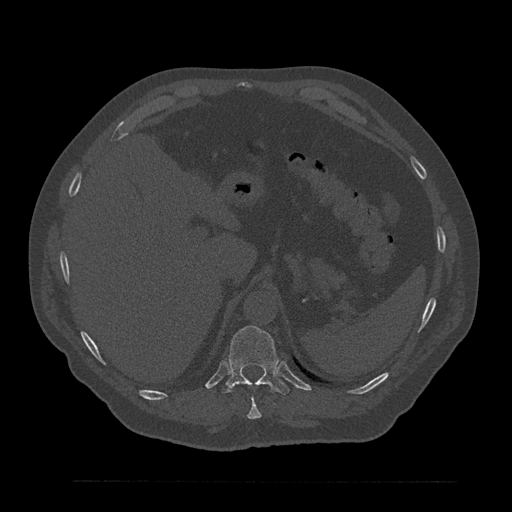
CT including the spine, one axial slice. Reconstruction kernel Br40s/3. Bone window (W 1800 / L 400 HU). 0.5 mm slice thickness. 512 × 512 image matrix, field of view 430 × 430 mm. Male patient, age 61 years. From the clinical record (not read from this slice): primary cancer: prostate.
Annotated regions visible in this slice (semi-automatically segmented with operator editing):
- T10 vertebra: bounding box (x1, y1, x2, y2) in pixels: (247, 397, 262, 419)
- T11 vertebra: (222, 326, 289, 395)